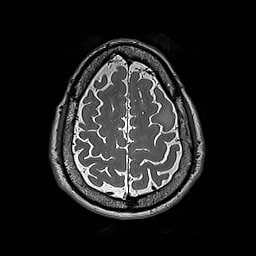
Brain MRI from a brain-tumour surgery series, one axial slice. 1 mm slice thickness. 256 × 256 image matrix, field of view 250 × 250 mm. Case-level facts recorded for this patient, not image findings: histopathology: Astrocytoma; WHO grade: 2; IDH mutation: yes; tumour location: Left Frontal.
Structures marked on this image (manually delineated by an expert):
- tumour: bounding box (x1, y1, x2, y2) in pixels: (158, 107, 172, 127)